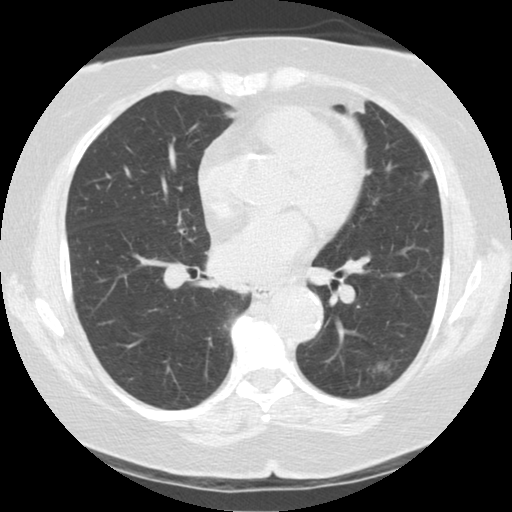
Low-dose screening chest CT, one axial slice; slice 66 of 122 in the series (ordered by position); reconstruction kernel STANDARD; 140 kVp; lung window (W 1500 / L -600 HU); 2.5 mm slice thickness; 512 × 512 image matrix.
Structures marked on this image (manually delineated by an expert):
- lesion 1 (tumor, lower lobe of left lung): bounding box <377,364,386,370> (left, top, right, bottom; pixels)